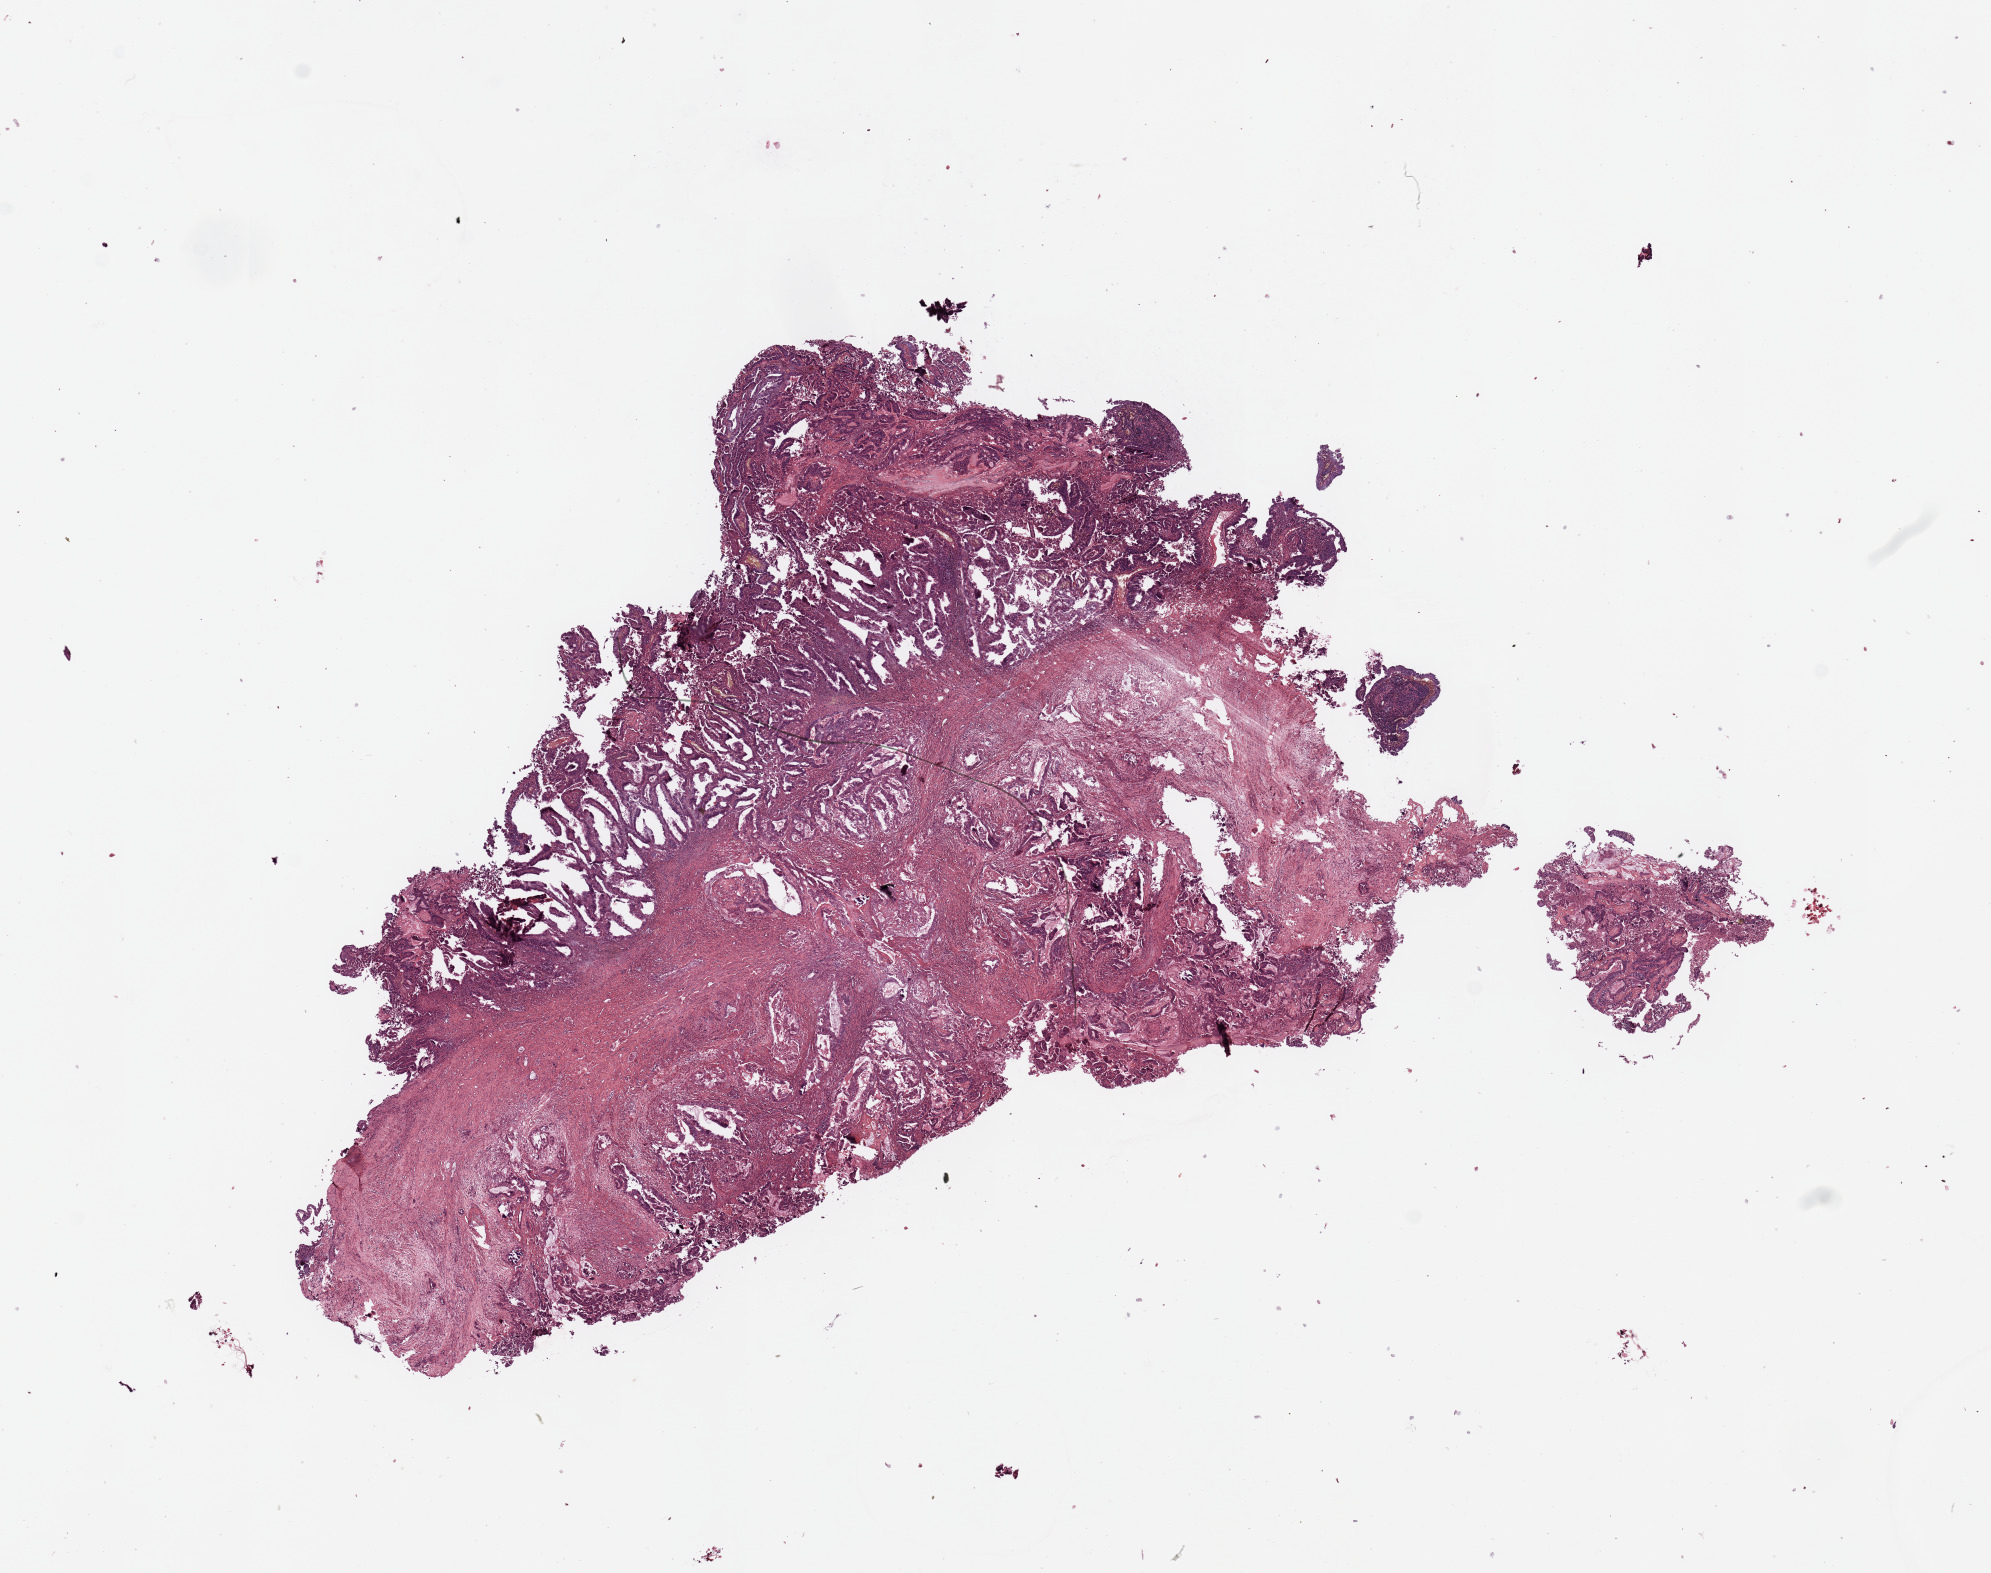
Whole-slide histology image, H&E-stained, low-resolution overview of the scanned area, about 15.8 x 12.4 mm (slide scanned at 20x). Tumour tissue sample, sampled site: uterus. 70-year-old female patient. Histologic grade: G3 (poorly differentiated). Pathologist review of this section (percent, as recorded): tumour nuclei 80%, necrosis 0%.
• AJCC pathologic stage: I
• diagnosis: Endometrioid adenocarcinoma, NOS